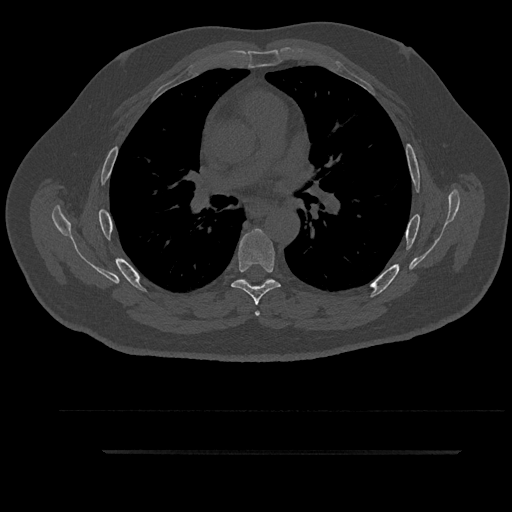
CT including the spine, one axial slice. Position 578 of 797 along the scan axis. Reconstruction kernel Br40s/3. 120 kVp. Bone window (W 1800 / L 400 HU). 0.5 mm slice thickness. 512 × 512 image matrix. Male patient, age 63 years. Case-level facts recorded for this patient, not image findings: primary cancer: renal.
Outlined on this slice (semi-automatic segmentation, software-assisted and operator-edited):
- T5 vertebra: bounding box [x1, y1, x2, y2] px = [238, 279, 271, 316]
- T6 vertebra: [231, 229, 281, 305]
- T7 vertebra: [242, 279, 270, 284]